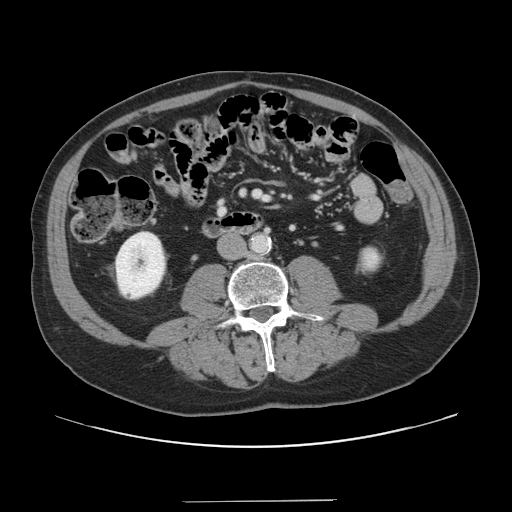
Contrast-enhanced abdominal CT, one axial slice; slice 25 of 151 in the series (ordered by position); 120 kVp; soft-tissue window (W 400 / L 40 HU); 512 × 512 image matrix. Male patient, age 63 years. Case-level facts recorded for this patient, not image findings: diagnosis: colorectal cancer liver metastases, imaged before liver resection.
Structures marked on this image (expert manual segmentation):
- portal vein (with intrahepatic branches): bounding box <254,191,267,200> (left, top, right, bottom; pixels)